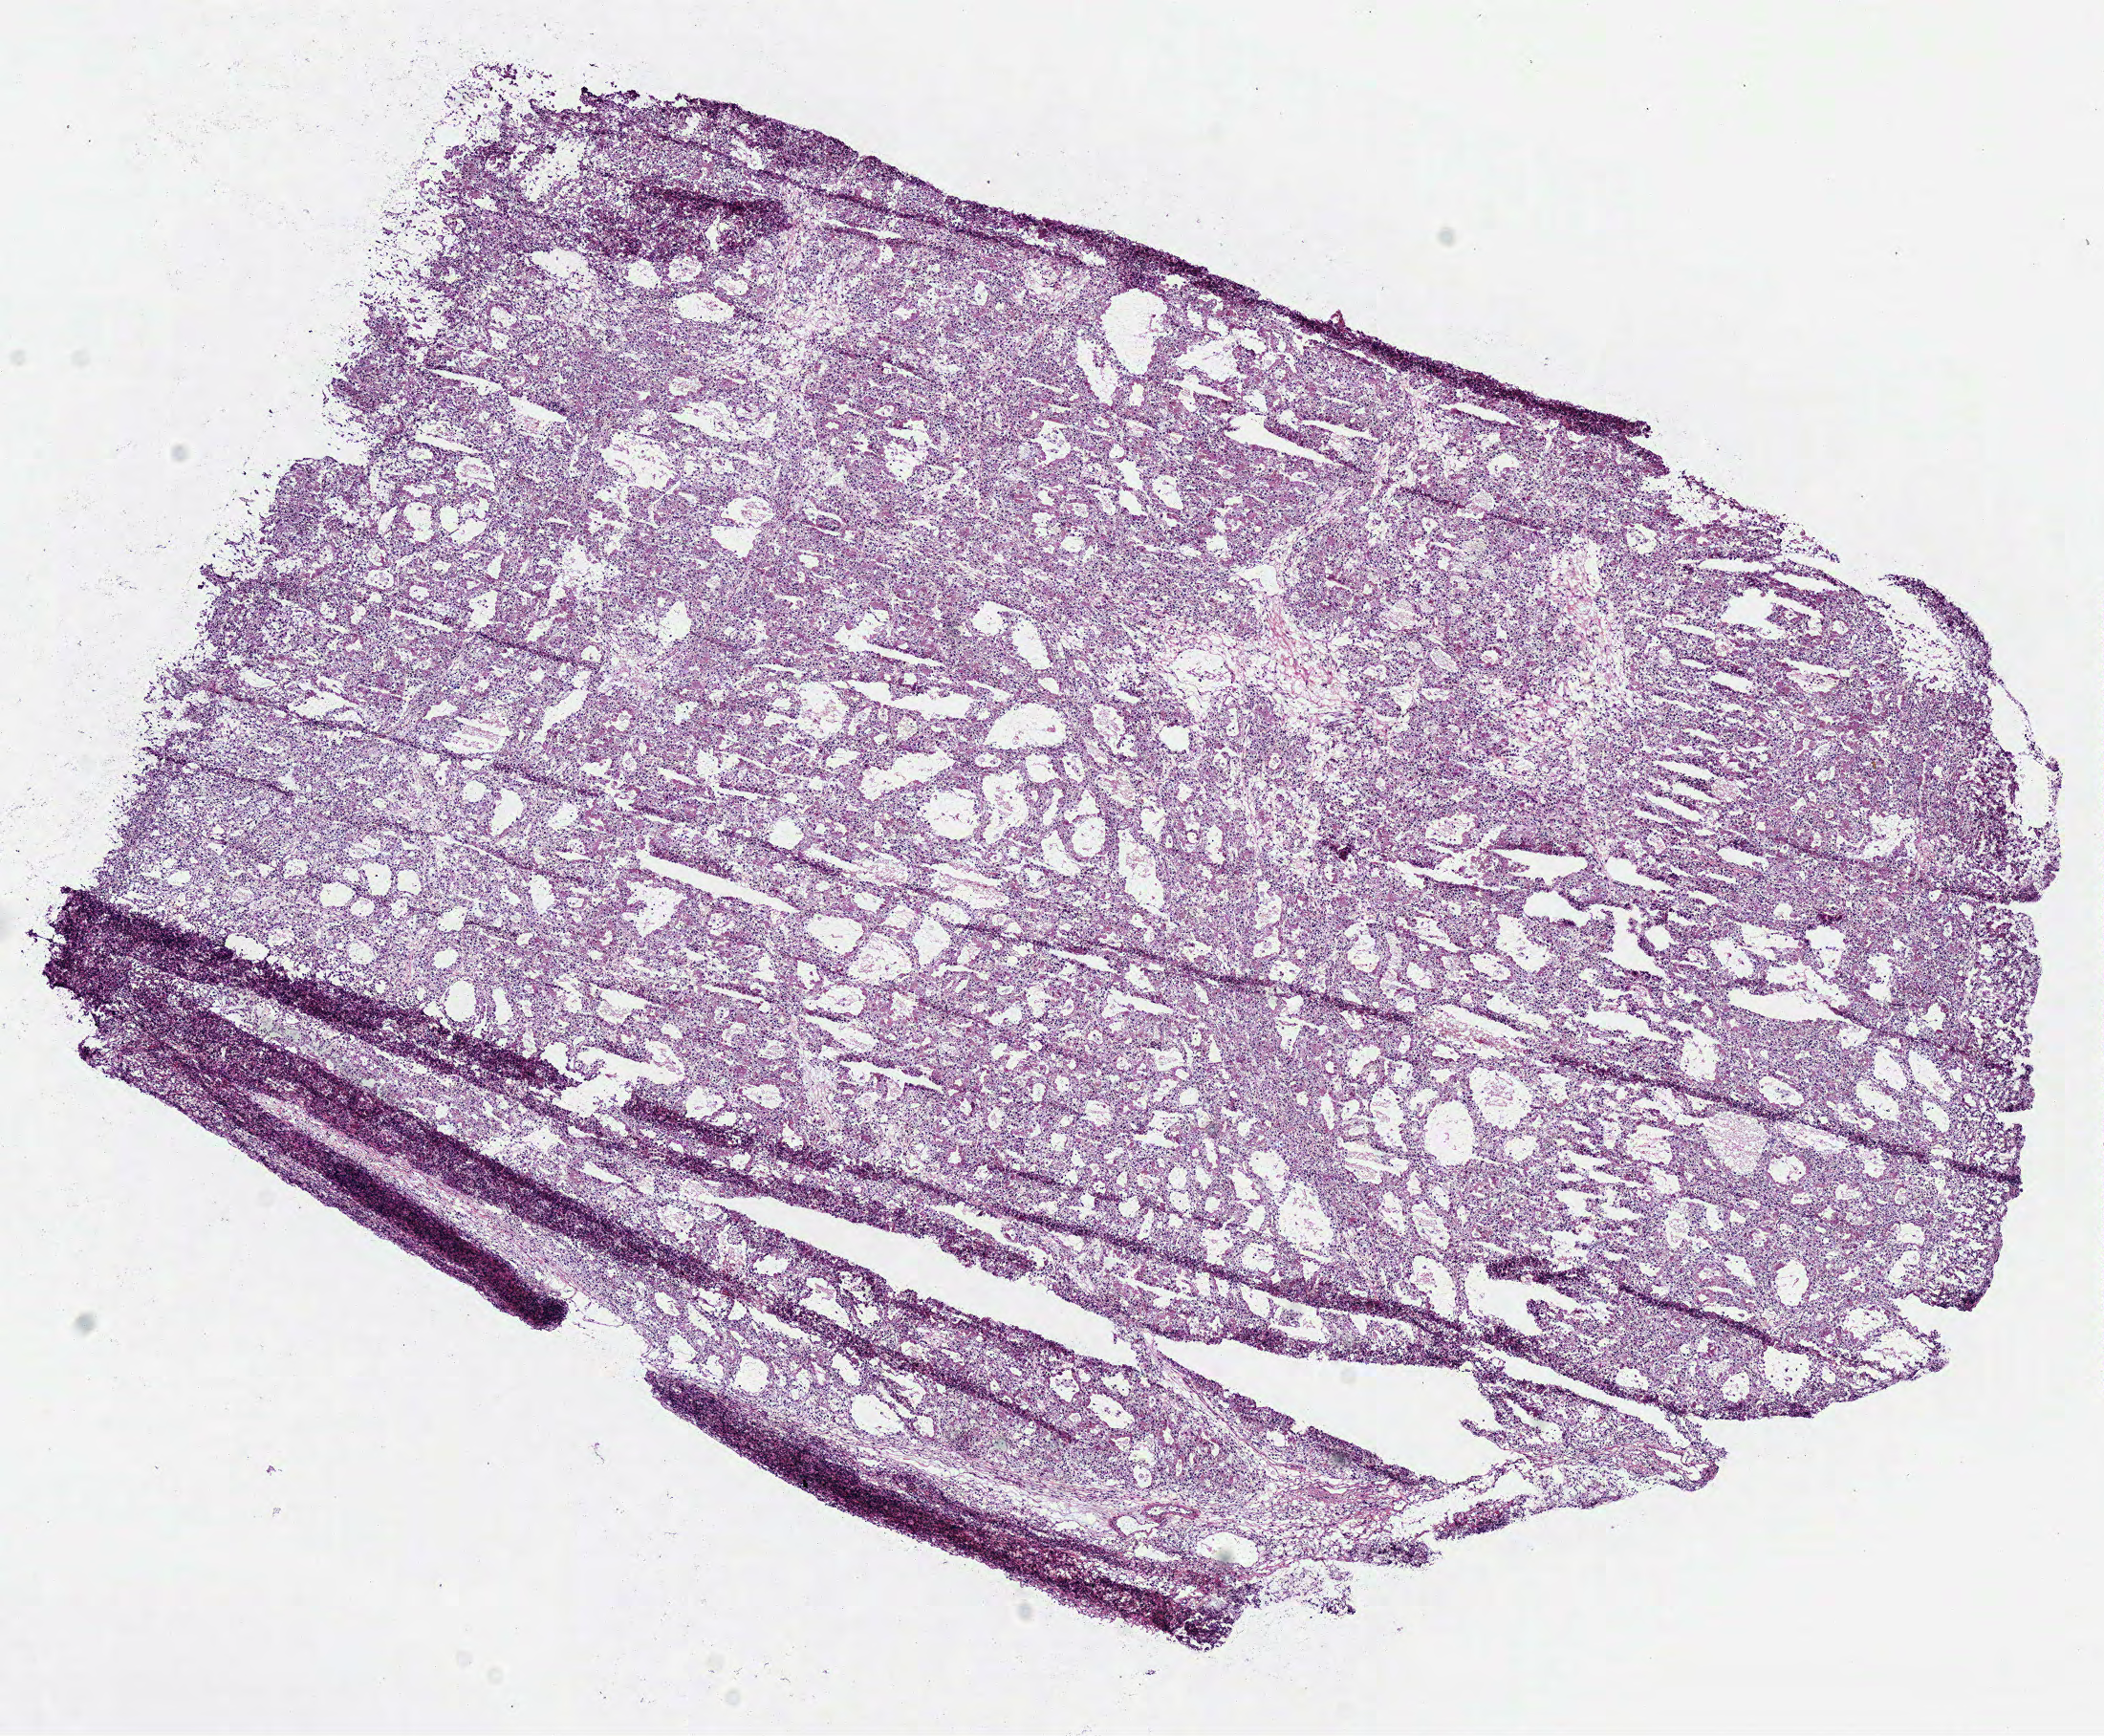
Digitized H&E-stained tissue section (whole slide), low-resolution overview of the scanned area, about 8.7 x 7.2 mm. Frozen section. Sample: primary tumour, kidney. Female, age 44 years at initial diagnosis. Histologic grade: G2 (moderately differentiated). Slide review estimates, as recorded: tumour cells 95%, tumour nuclei 85%, normal cells 0%, stromal cells 5%, necrosis 0%.
• pathologic diagnosis: Clear cell adenocarcinoma, NOS
• AJCC pathologic stage: I